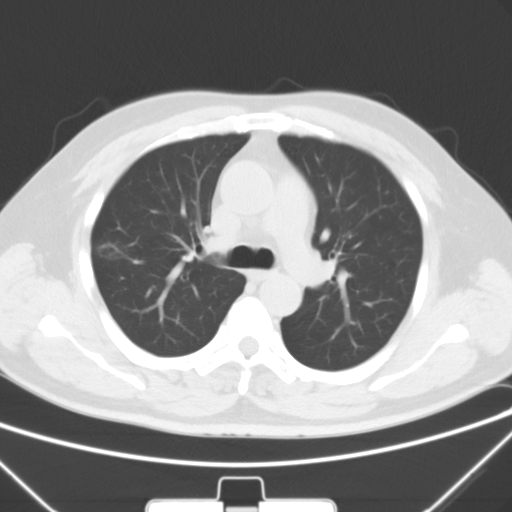
Chest CT, one axial slice; position 41 of 64 along the scan axis; 120 kVp; lung window (W 1500 / L -600 HU); 5 mm slice thickness; 512 × 512 image matrix, field of view 350 × 350 mm. Male patient, age 58 years. Case-level facts recorded for this patient, not image findings: clinical TNM (as recorded): T1c N0 M0; histopathological grade: G2.
Annotated regions visible in this slice (bounding box drawn by a radiologist):
- lung tumour (recorded histology: adenocarcinoma): box from (x=90, y=235) to (x=134, y=270) px